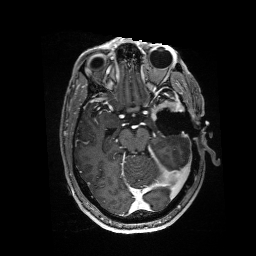
Brain MRI from a brain-tumour surgery series, one axial slice. Slice 101 of 176 in the series (ordered by position). T1-weighted post-contrast. 1 mm slice thickness. 256 × 256 image matrix, field of view 256 × 256 mm. From the clinical record (not read from this slice): histopathology: Glioblastoma; WHO grade: 4; IDH mutation: no.
Annotated regions visible in this slice (manually delineated by an expert):
- residual tumour: bounding box [x1, y1, x2, y2] px = [151, 101, 185, 120]